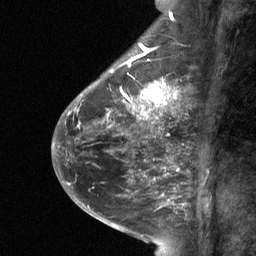
Breast MRI (dynamic contrast-enhanced), one sagittal slice; slice 23 of 64 in the series (ordered by position); dynamic contrast-enhanced study with each time point stored as its own series, time point 2 of 3 at this slice position (early post-contrast, ordered by acquisition time); 1.5 T; TE 4.8 ms, TR 27 ms; 2 mm slice thickness; 256 × 256 image matrix, field of view 180 × 180 mm. Female patient, age 59 years. From the clinical record (not read from this slice): setting: breast cancer imaged before/during neoadjuvant chemotherapy; receptor status: triple-negative.
Annotated regions visible in this slice (semi-automatic segmentation, software-assisted and operator-edited):
- analysis volume of interest (the breast-tissue region the enhancement analysis was run in; not a lesion): box from (x=113, y=78) to (x=175, y=120) px
- tumour enhancement mask (voxels above the 90 % enhancement threshold inside the analysis volume of interest): (x=123, y=81)–(x=175, y=119)